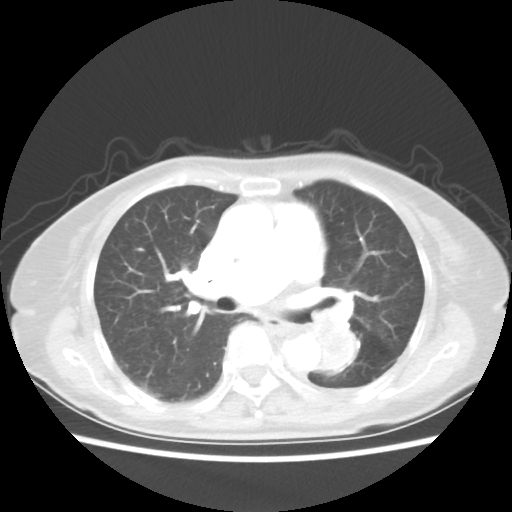
Chest CT, one axial slice. Position 28 of 50 along the scan axis. Reconstruction kernel STANDARD. Lung window (W 1500 / L -600 HU). 512 × 512 image matrix, field of view 335 × 335 mm. Patient: female, 81 years. From the clinical record (not read from this slice): clinical TNM (as recorded): T2 N0 M1a.
Annotated regions visible in this slice (rectangle marked by the reading radiologist):
- lung tumour (recorded histology: squamous cell carcinoma): box from (x=305, y=313) to (x=366, y=383) px